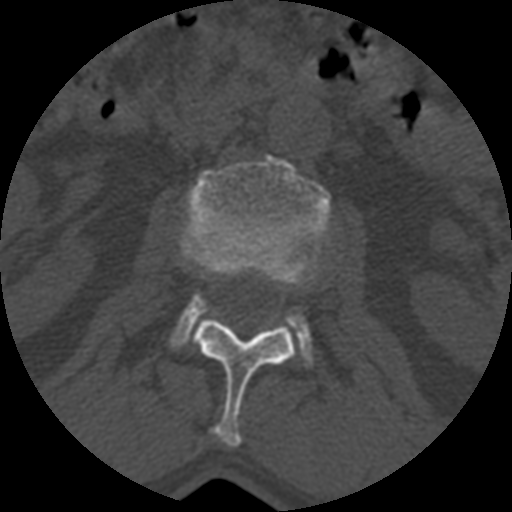
CT including the spine, one axial slice; slice 349 of 399 in the series (ordered by position); reconstruction kernel STANDARD; 120 kVp; bone window (W 1800 / L 400 HU); 512 × 512 image matrix, field of view 160 × 160 mm. Patient age 71 years. From the clinical record (not read from this slice): primary cancer: prostate.
Annotated regions visible in this slice (semi-automatic segmentation, software-assisted and operator-edited):
- L1 vertebra: box from (x=195, y=318) to (x=294, y=446) px
- L2 vertebra: (x=169, y=156)–(x=332, y=370)